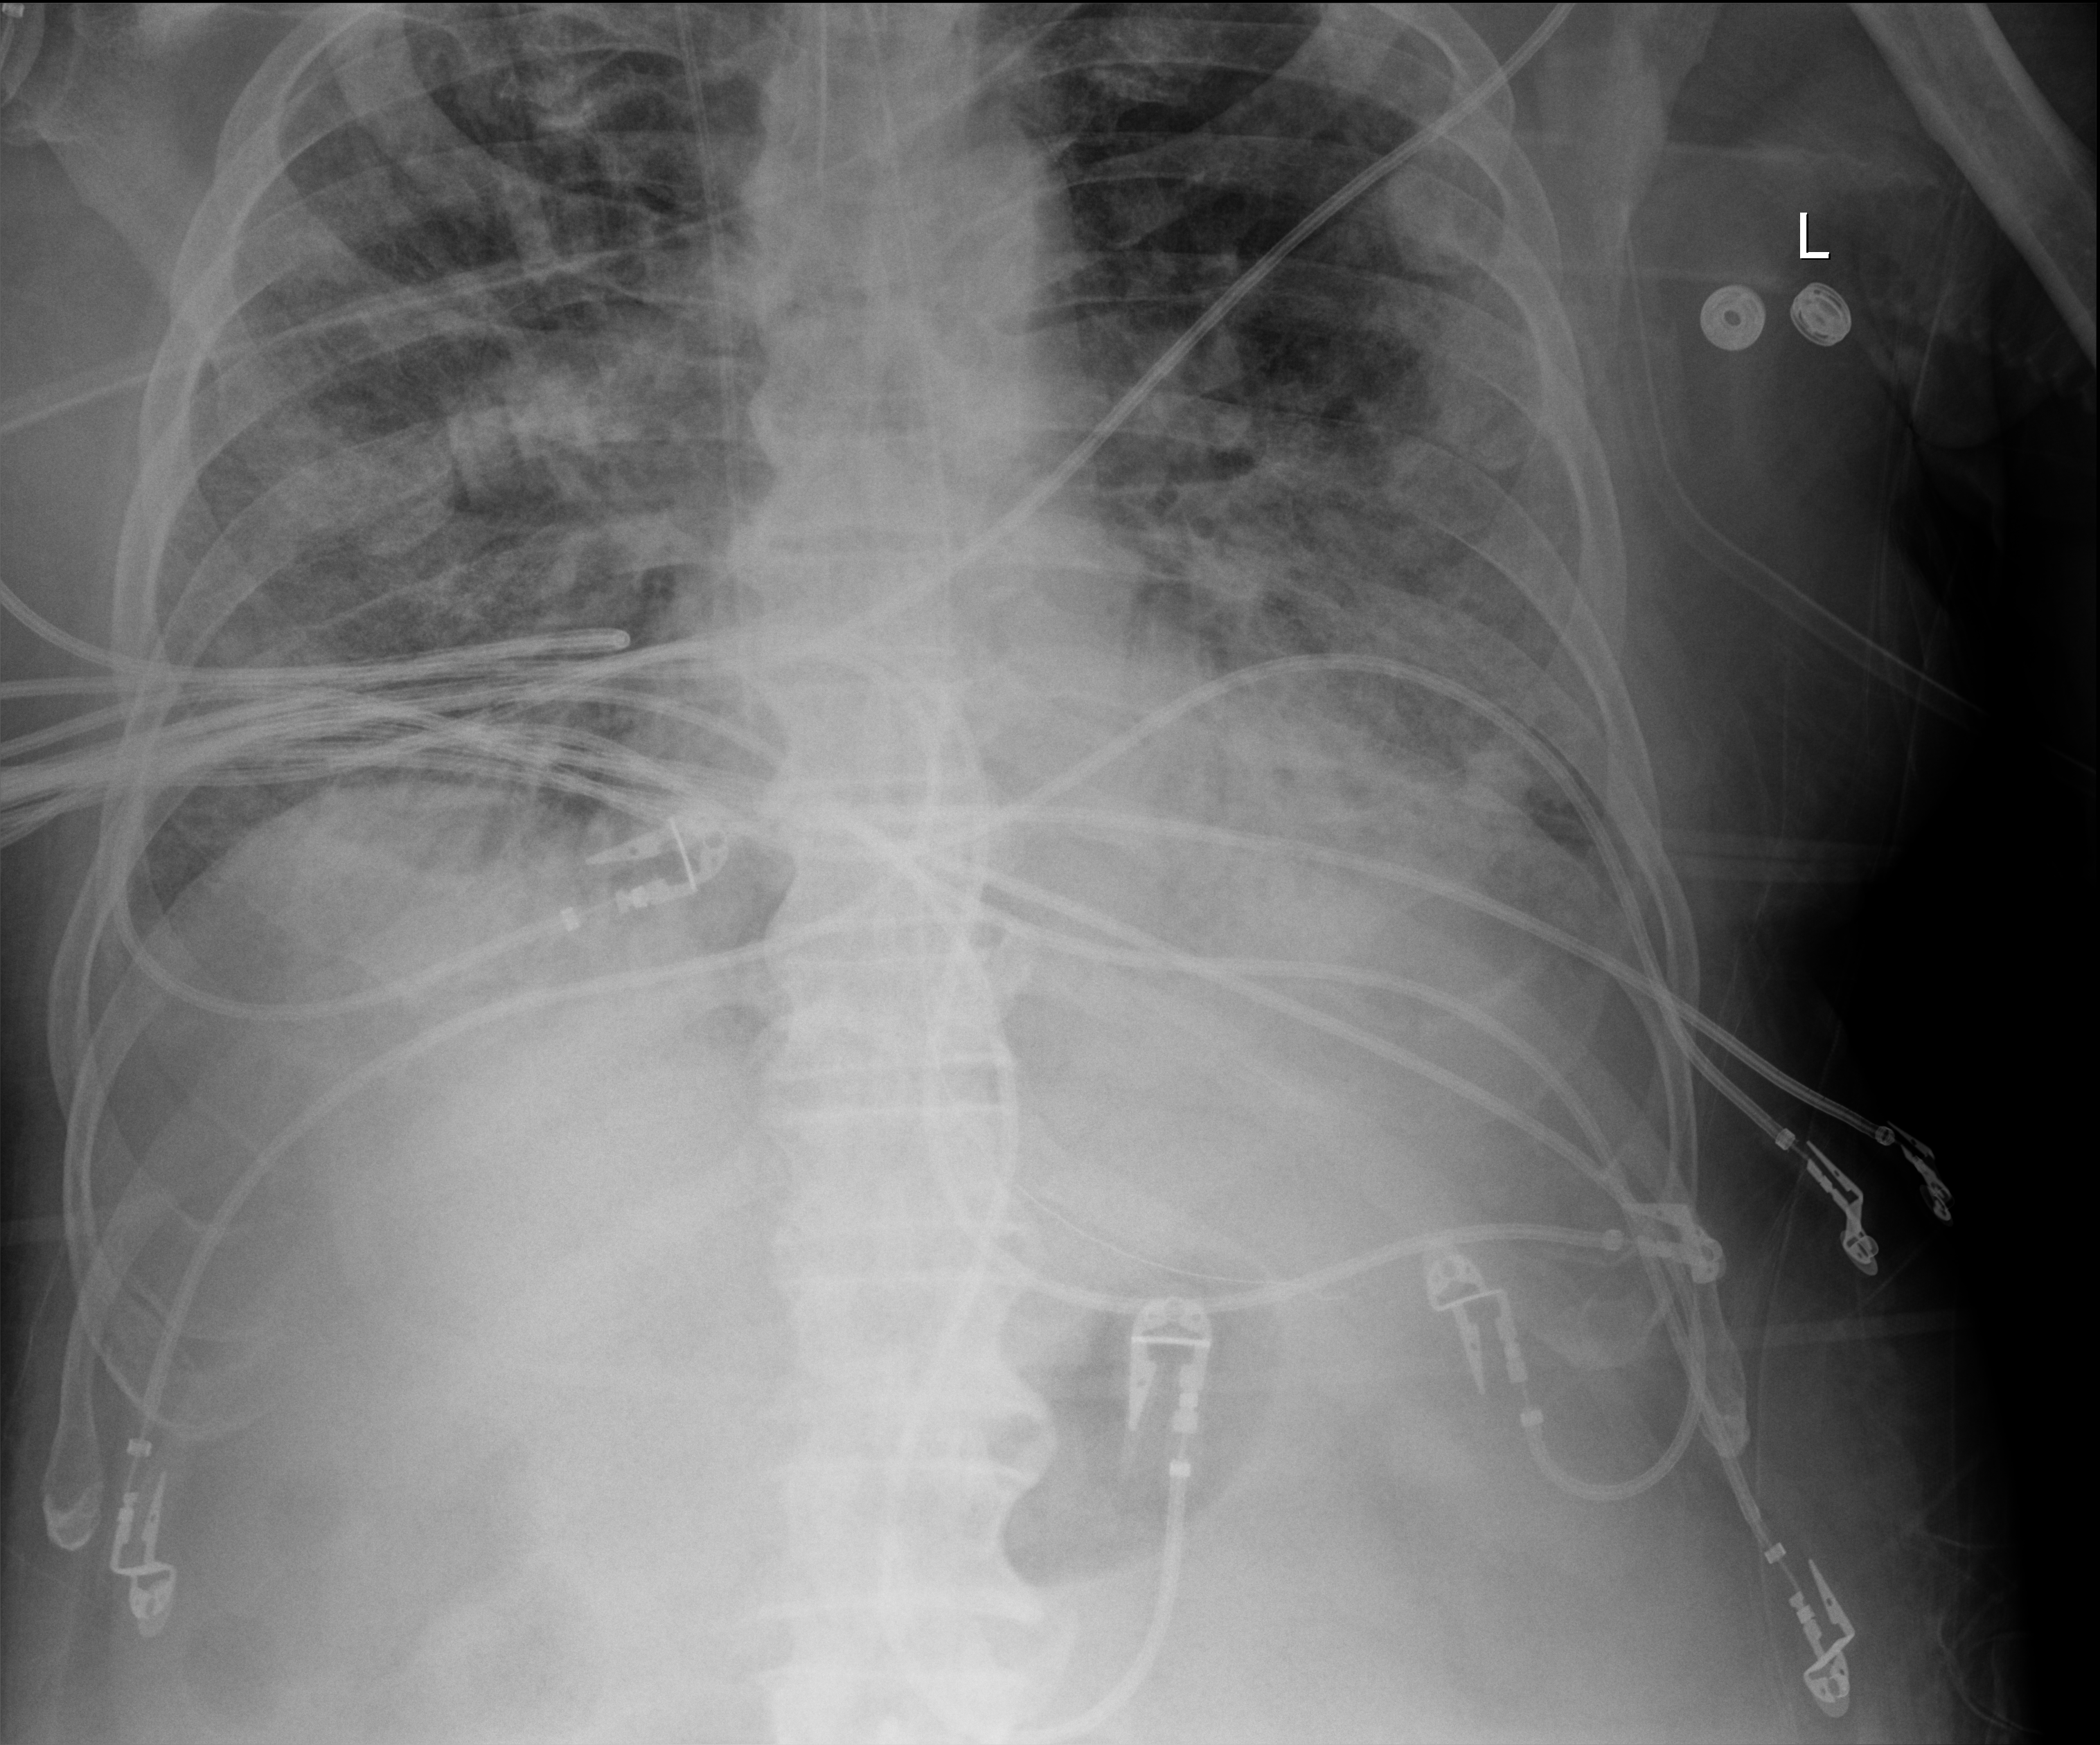
Chest X-ray (portable); anteroposterior (AP) projection. Male patient hospitalised with COVID-19, age 75–90 years.
Admission-level facts for this patient (not findings on this image; timing relative to this image not recorded): COPD (admission record): no; mechanically ventilated during this hospital stay: yes.